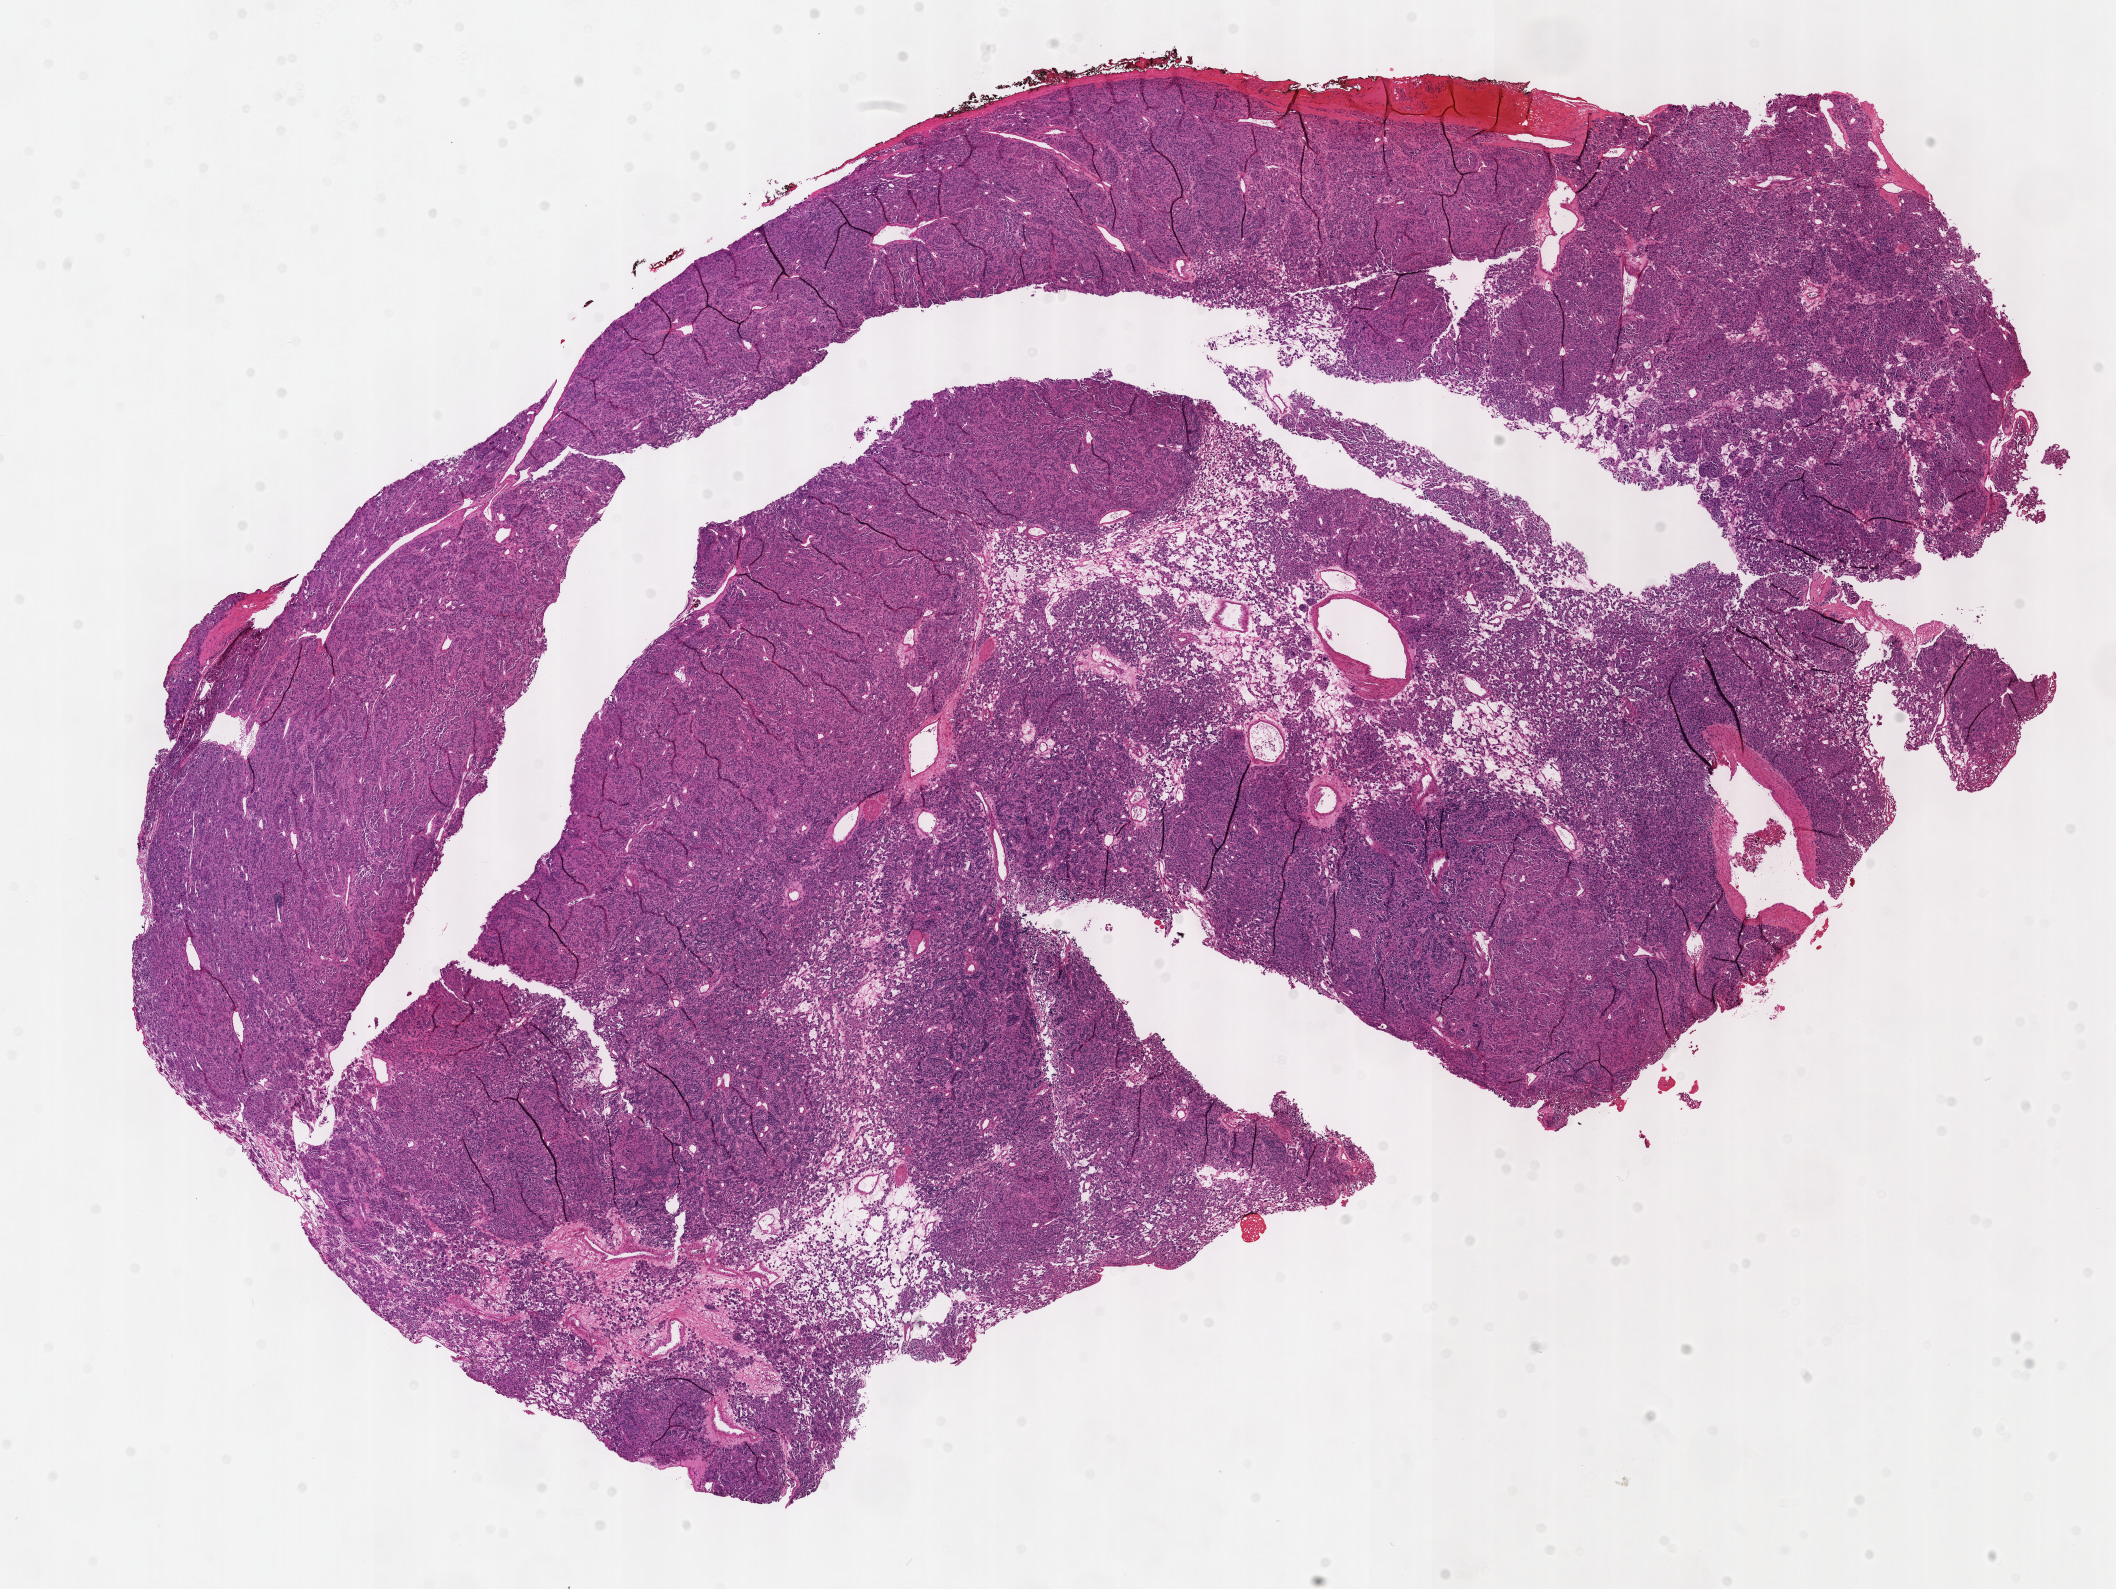
Digitized Hematoxylin and eosin (H&E) stained tissue section (whole slide), whole scanned area (about 17.1 x 12.9 mm, acquisition: 40x scan) shown as a low-resolution overview; formalin-fixed paraffin-embedded (FFPE) diagnostic section; primary tumour sample from the connective, subcutaneous and other soft tissues. Male, age 27 years at initial diagnosis.
• pathologic diagnosis: Extra-adrenal paraganglioma, NOS (connective, subcutaneous and other soft tissues of trunk, NOS)